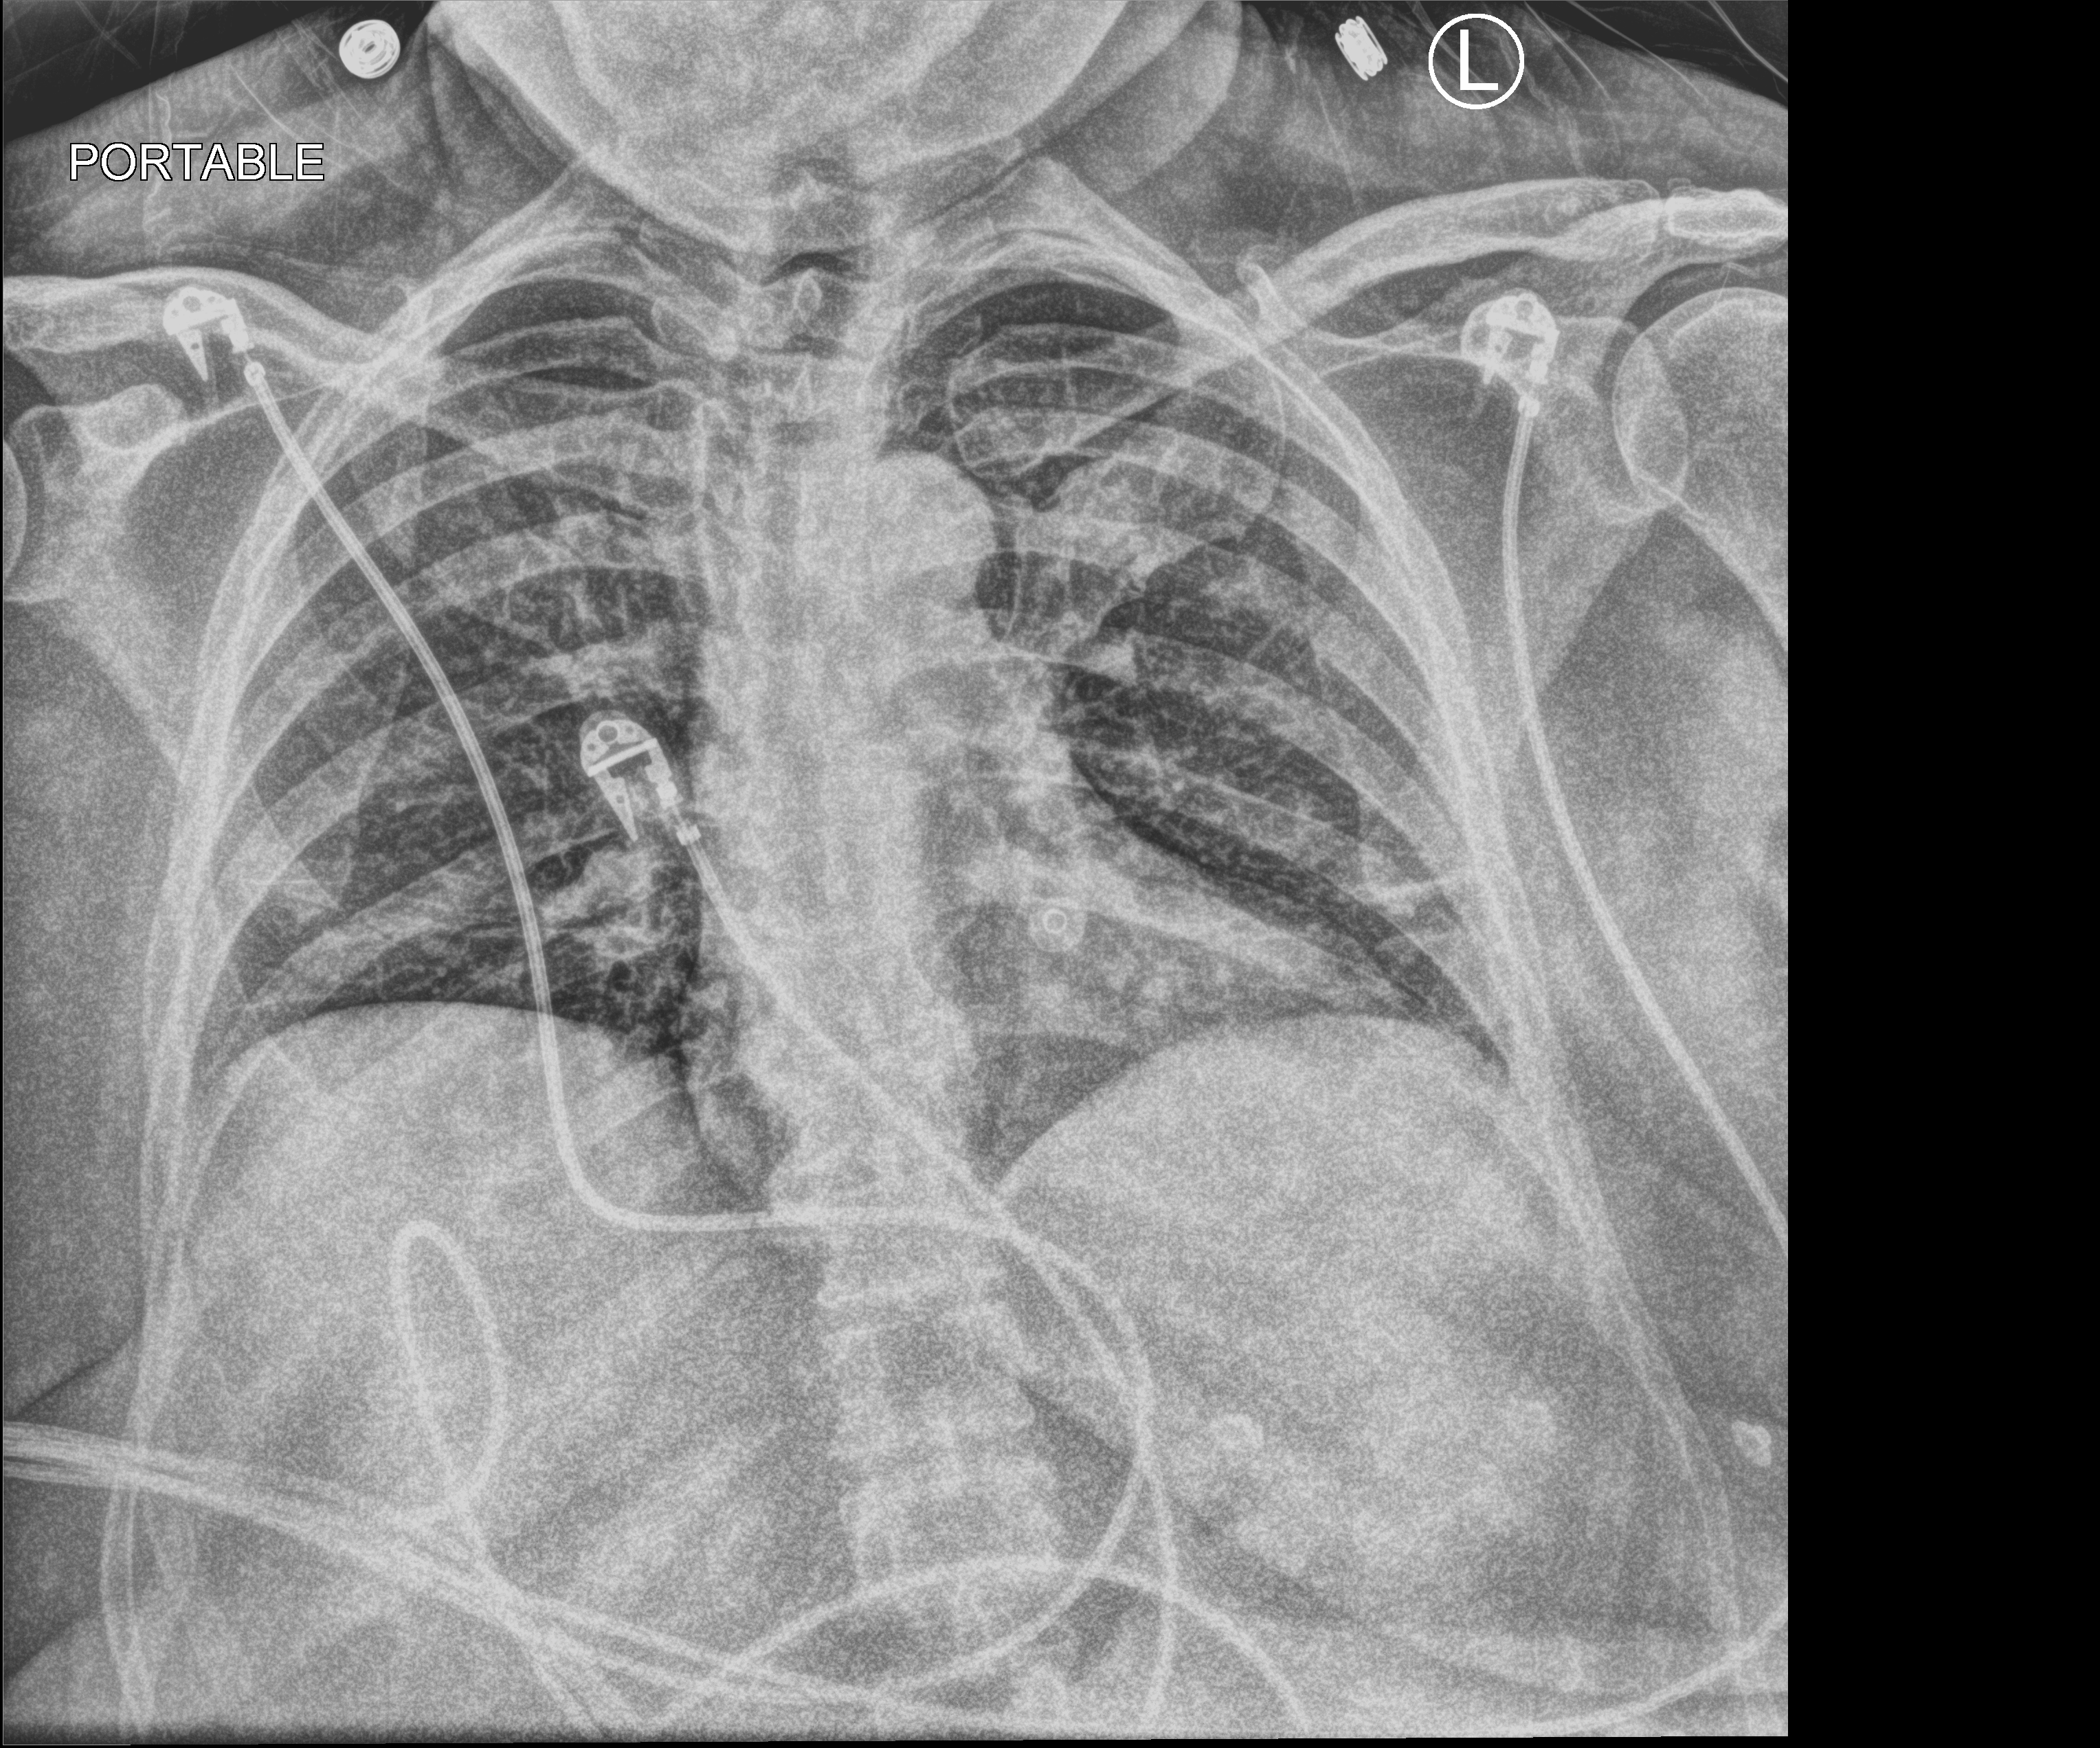
Chest X-ray (portable). Female patient hospitalised with COVID-19, age 60–74 years.
Hospital-stay facts (about this admission, not read from this image; timing relative to this image not recorded): admitted to intensive care during this hospital stay: yes.